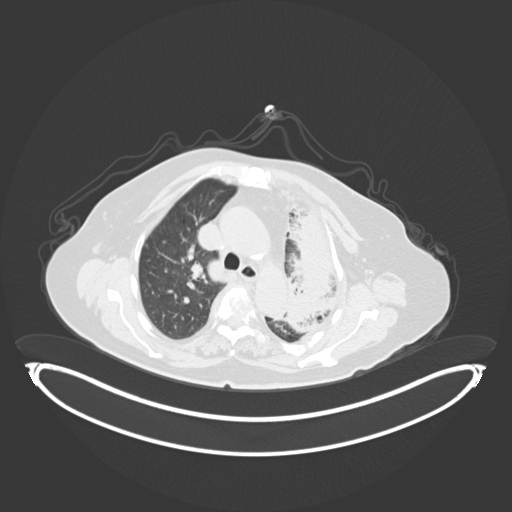
Chest CT, one axial slice; position 216 of 284 along the scan axis; lung window (W 1500 / L -600 HU); 3 mm slice thickness; 512 × 512 image matrix, field of view 500 × 500 mm. Female patient, age 75 years. Case-level facts recorded for this patient, not image findings: clinical TNM (as recorded): T3 N3 M1.
Structures marked on this image (bounding box drawn by a radiologist):
- lung tumour (recorded histology: adenocarcinoma): bounding box (x1, y1, x2, y2) in pixels: (269, 205, 336, 336)